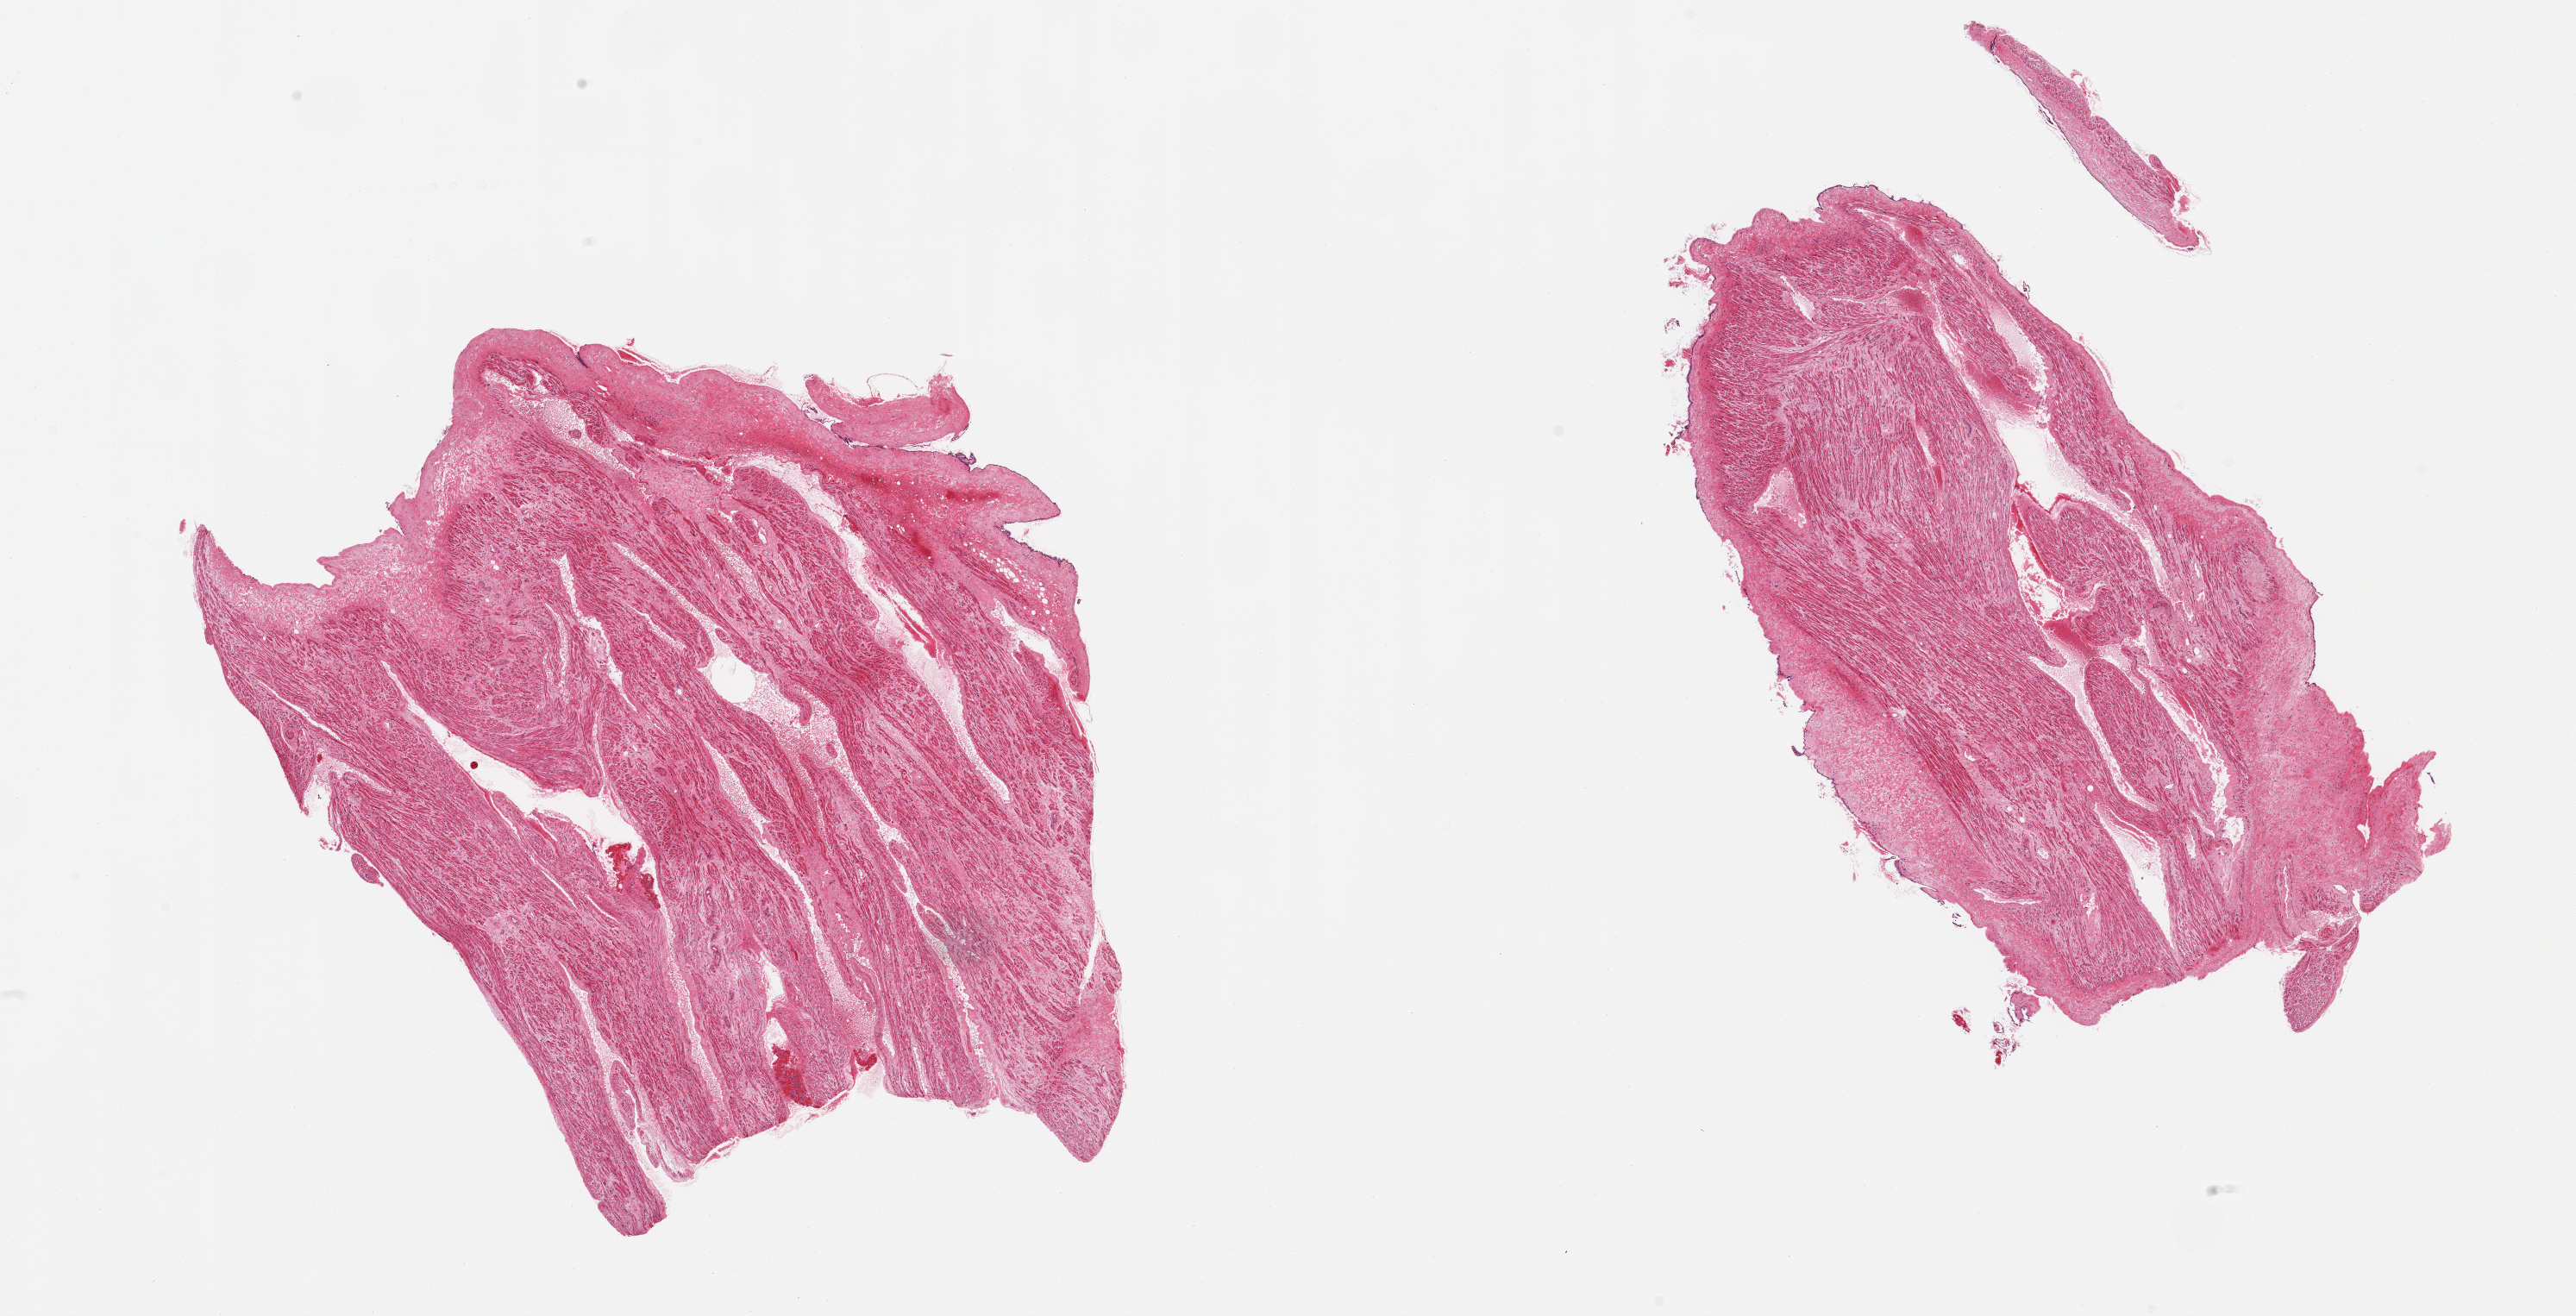
Whole-slide image, H&E stain — low-resolution overview of the scanned area, about 23.6 x 12.1 mm, PAXgene-fixed, paraffin-embedded tissue, sampled site (target tissue): auricular appendage, tissue donor sample. Donor sex: male.
Review note (as recorded): pieces.